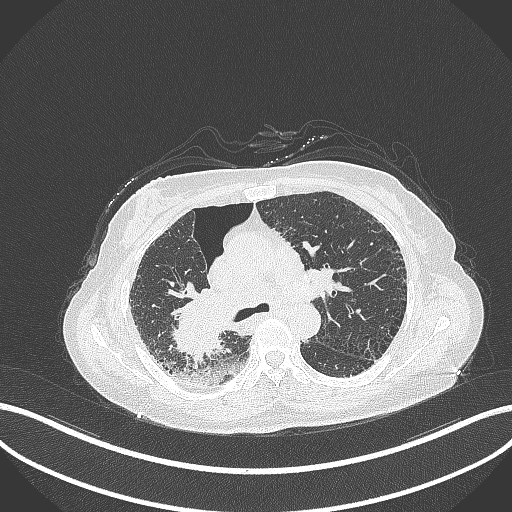
Chest CT, one axial slice. Slice 222 of 408 in the series (ordered by position). Reconstruction kernel B70f. Lung window (W 1500 / L -600 HU). 512 × 512 image matrix, field of view 400 × 400 mm. Female patient, age 64 years. Case-level facts recorded for this patient, not image findings: clinical TNM (as recorded): T3 N3 M0.
Structures marked on this image (bounding box drawn by a radiologist):
- lung tumour (recorded histology: squamous cell carcinoma): bounding box (x1, y1, x2, y2) in pixels: (163, 286, 231, 370)